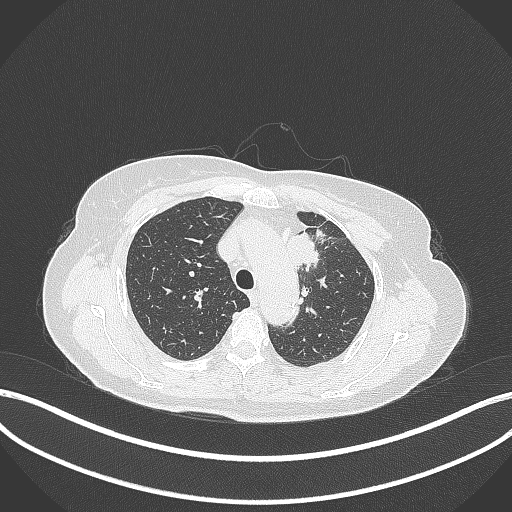
Chest CT, one axial slice. Position 252 of 369 along the scan axis. Lung window (W 1500 / L -600 HU). 1 mm slice thickness. 512 × 512 image matrix. Female patient, age 65 years. From the clinical record (not read from this slice): clinical TNM (as recorded): T2a N0 M0.
Outlined on this slice (rectangle marked by the reading radiologist):
- lung tumour (recorded histology: adenocarcinoma): bounding box [x1, y1, x2, y2] px = [291, 227, 327, 271]